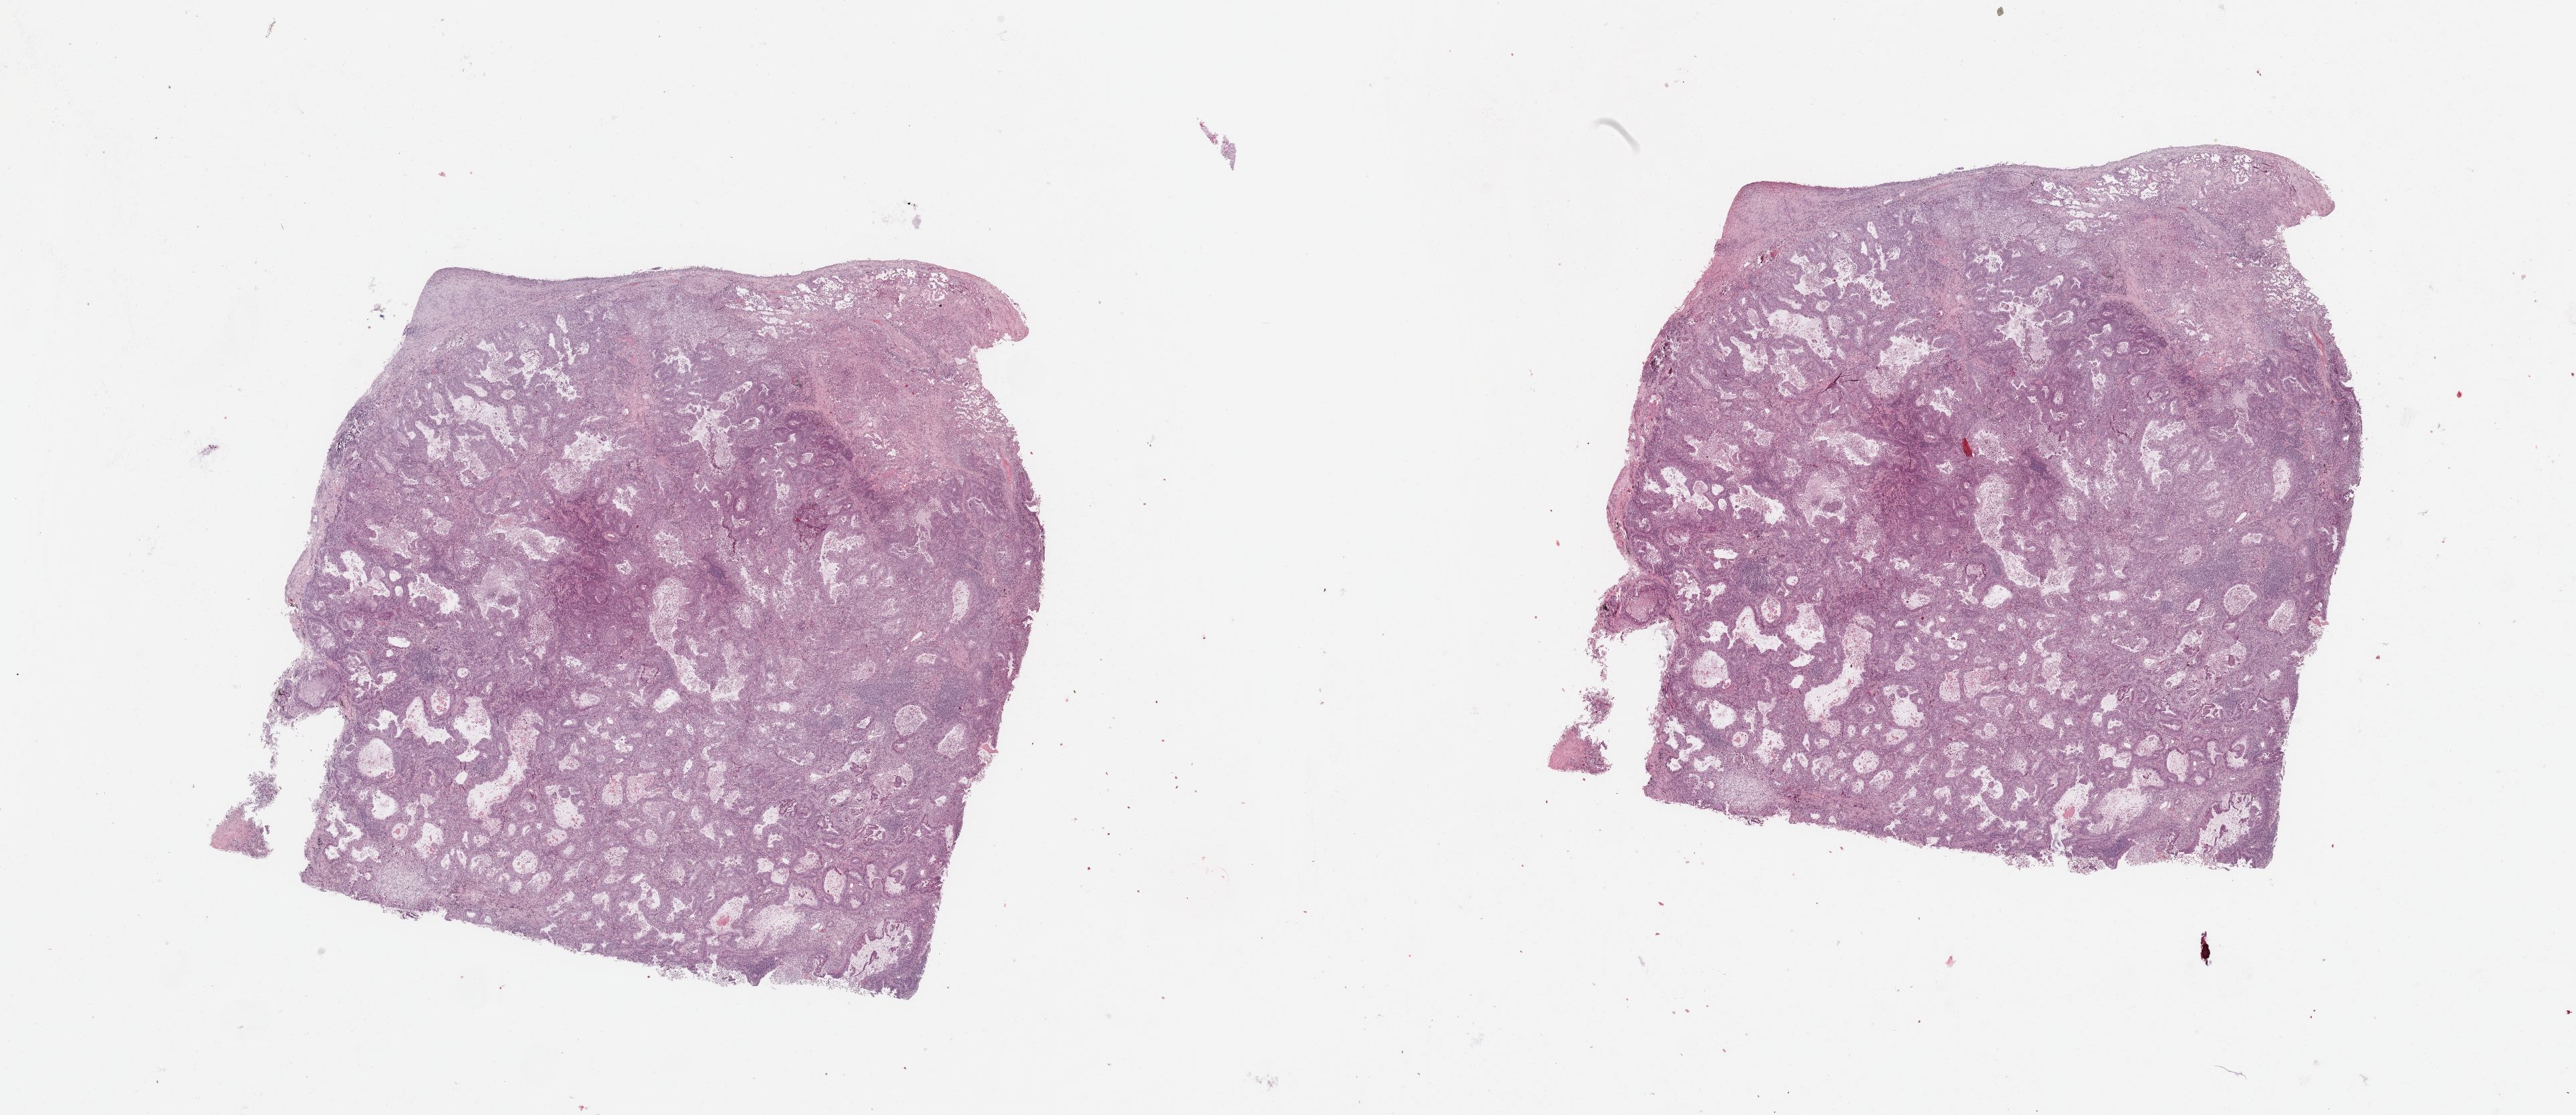
Whole-slide histology image, H&E-stained, low-resolution overview of the scanned area, about 30.5 x 13.2 mm (from a 20x scan). Lung, tissue type not recorded.
* patient diagnosis (cohort enrolment): lung adenocarcinoma (lung)